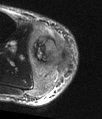
MRI of an extremity soft-tissue mass, one axial slice; position 18 of 48 along the scan axis; T2-weighted fat-saturated; MR volume resampled by the dataset authors to the PET/CT grid (not the native acquisition matrix); 102 × 119 image matrix. Male patient. From the clinical record (not read from this slice): histological type: pleiomorphic liposarcoma; grade: high; site of the primary tumour: right calf.
Annotated regions visible in this slice (expert contour drawn on MRI and transferred to this co-registered scan by the dataset authors):
- gross tumour volume including surrounding oedema: bounding box [x1, y1, x2, y2] px = [28, 26, 72, 97]
- gross tumour volume (mass): [32, 35, 72, 74]